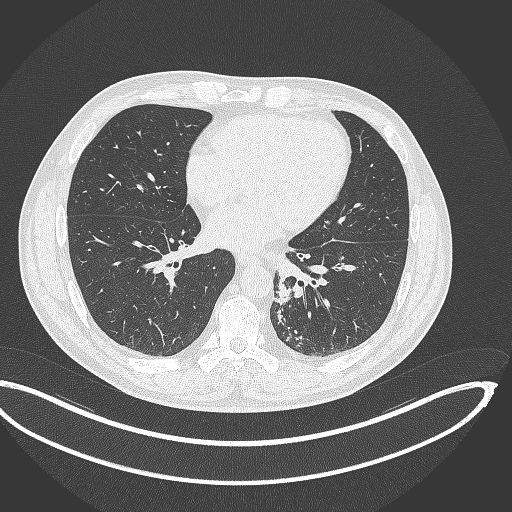
Chest CT, one axial slice. Position 141 of 362 along the scan axis. 120 kVp. Lung window (W 1500 / L -600 HU). 1 mm slice thickness. 512 × 512 image matrix, field of view 442 × 442 mm. Patient: male, 50 years. From the clinical record (not read from this slice): clinical TNM (as recorded): T2a N3 M0.
Annotated regions visible in this slice (rectangle marked by the reading radiologist):
- lung tumour (recorded histology: squamous cell carcinoma): bounding box (x1, y1, x2, y2) in pixels: (273, 277, 292, 306)